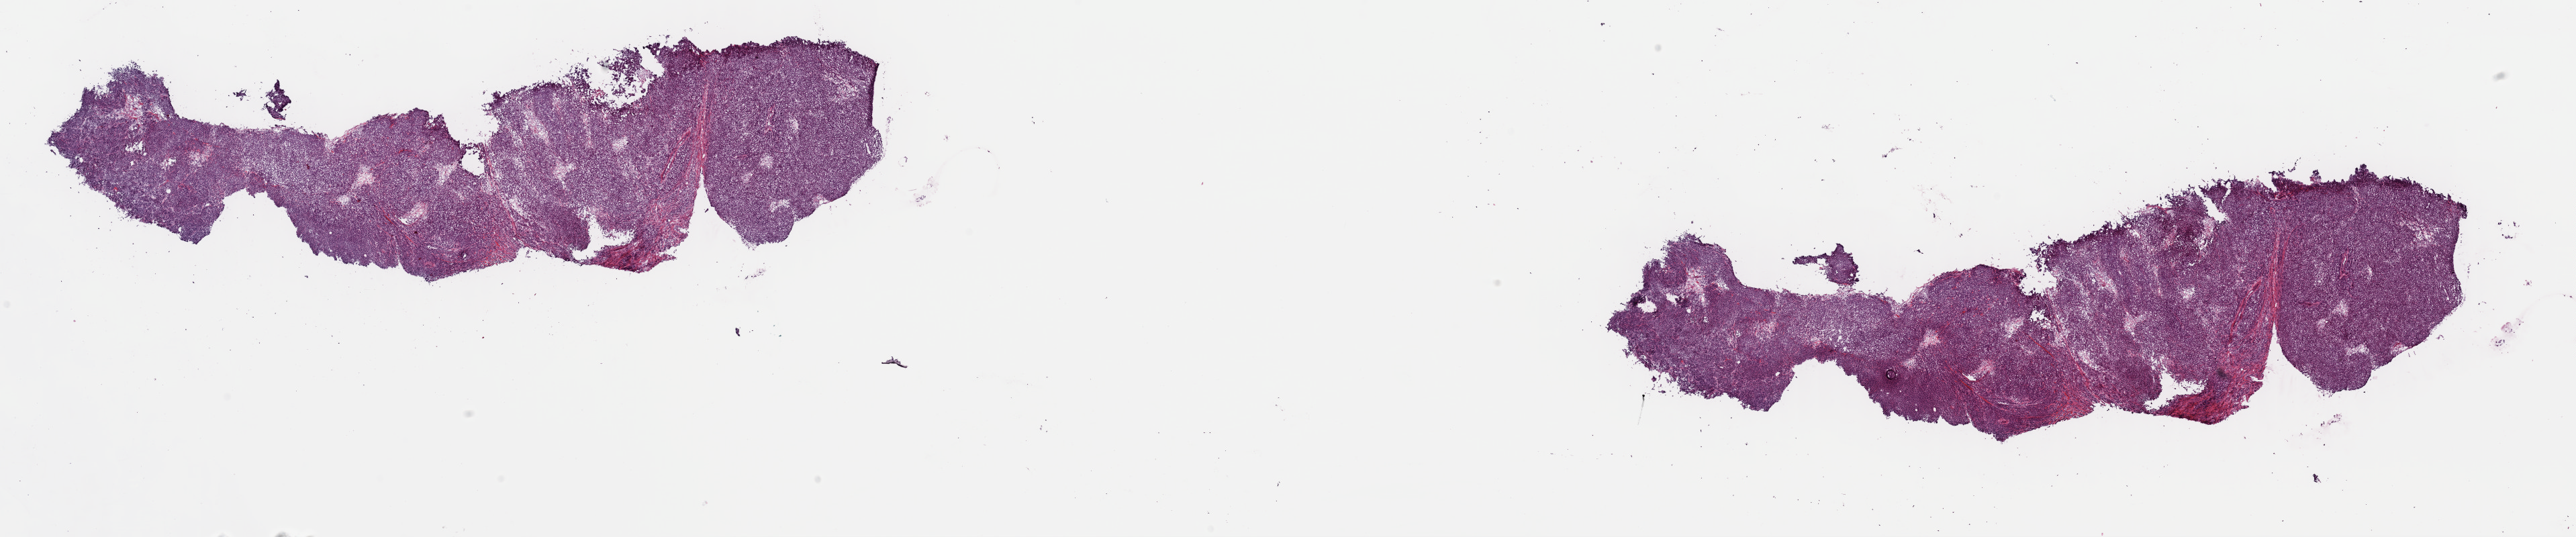
H&E-stained whole-slide image, a low-resolution overview of the entire scanned area, about 30.3 x 6.3 mm (from a 40x scan), frozen section from the top of the tissue portion, metastatic tumour sample. Male patient; age at initial diagnosis 72 years. Slide review estimates, as recorded: tumour cells 80%, tumour nuclei 85%, normal cells 0%, stromal cells 15%, necrosis 5%. Inflammatory infiltration, as recorded: lymphocyte infiltration 2%, monocyte infiltration 0%, neutrophil infiltration 0%.
This section: metastatic tumour tissue. Patient diagnosis: Malignant melanoma, NOS.